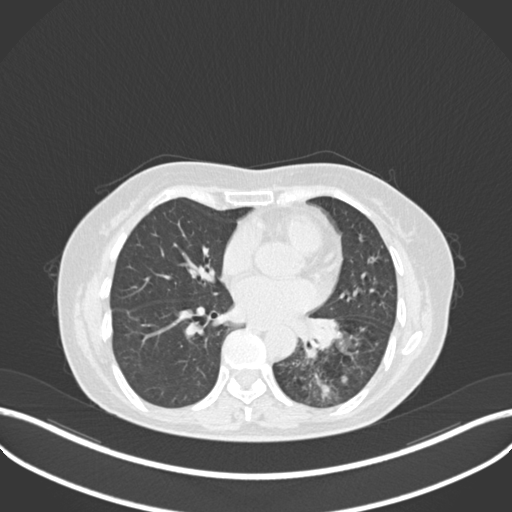
Chest CT, one axial slice. Position 117 of 270 along the scan axis. Reconstruction kernel B30f. 120 kVp. Lung window (W 1500 / L -600 HU). 1 mm slice thickness. 512 × 512 image matrix. Patient: female, 63 years. Case-level facts recorded for this patient, not image findings: clinical TNM (as recorded): T1b N0 M0; histopathological grade: G2-3.
Outlined on this slice (bounding box drawn by a radiologist):
- lung tumour (recorded histology: adenocarcinoma): bounding box <292,310,350,364> (left, top, right, bottom; pixels)